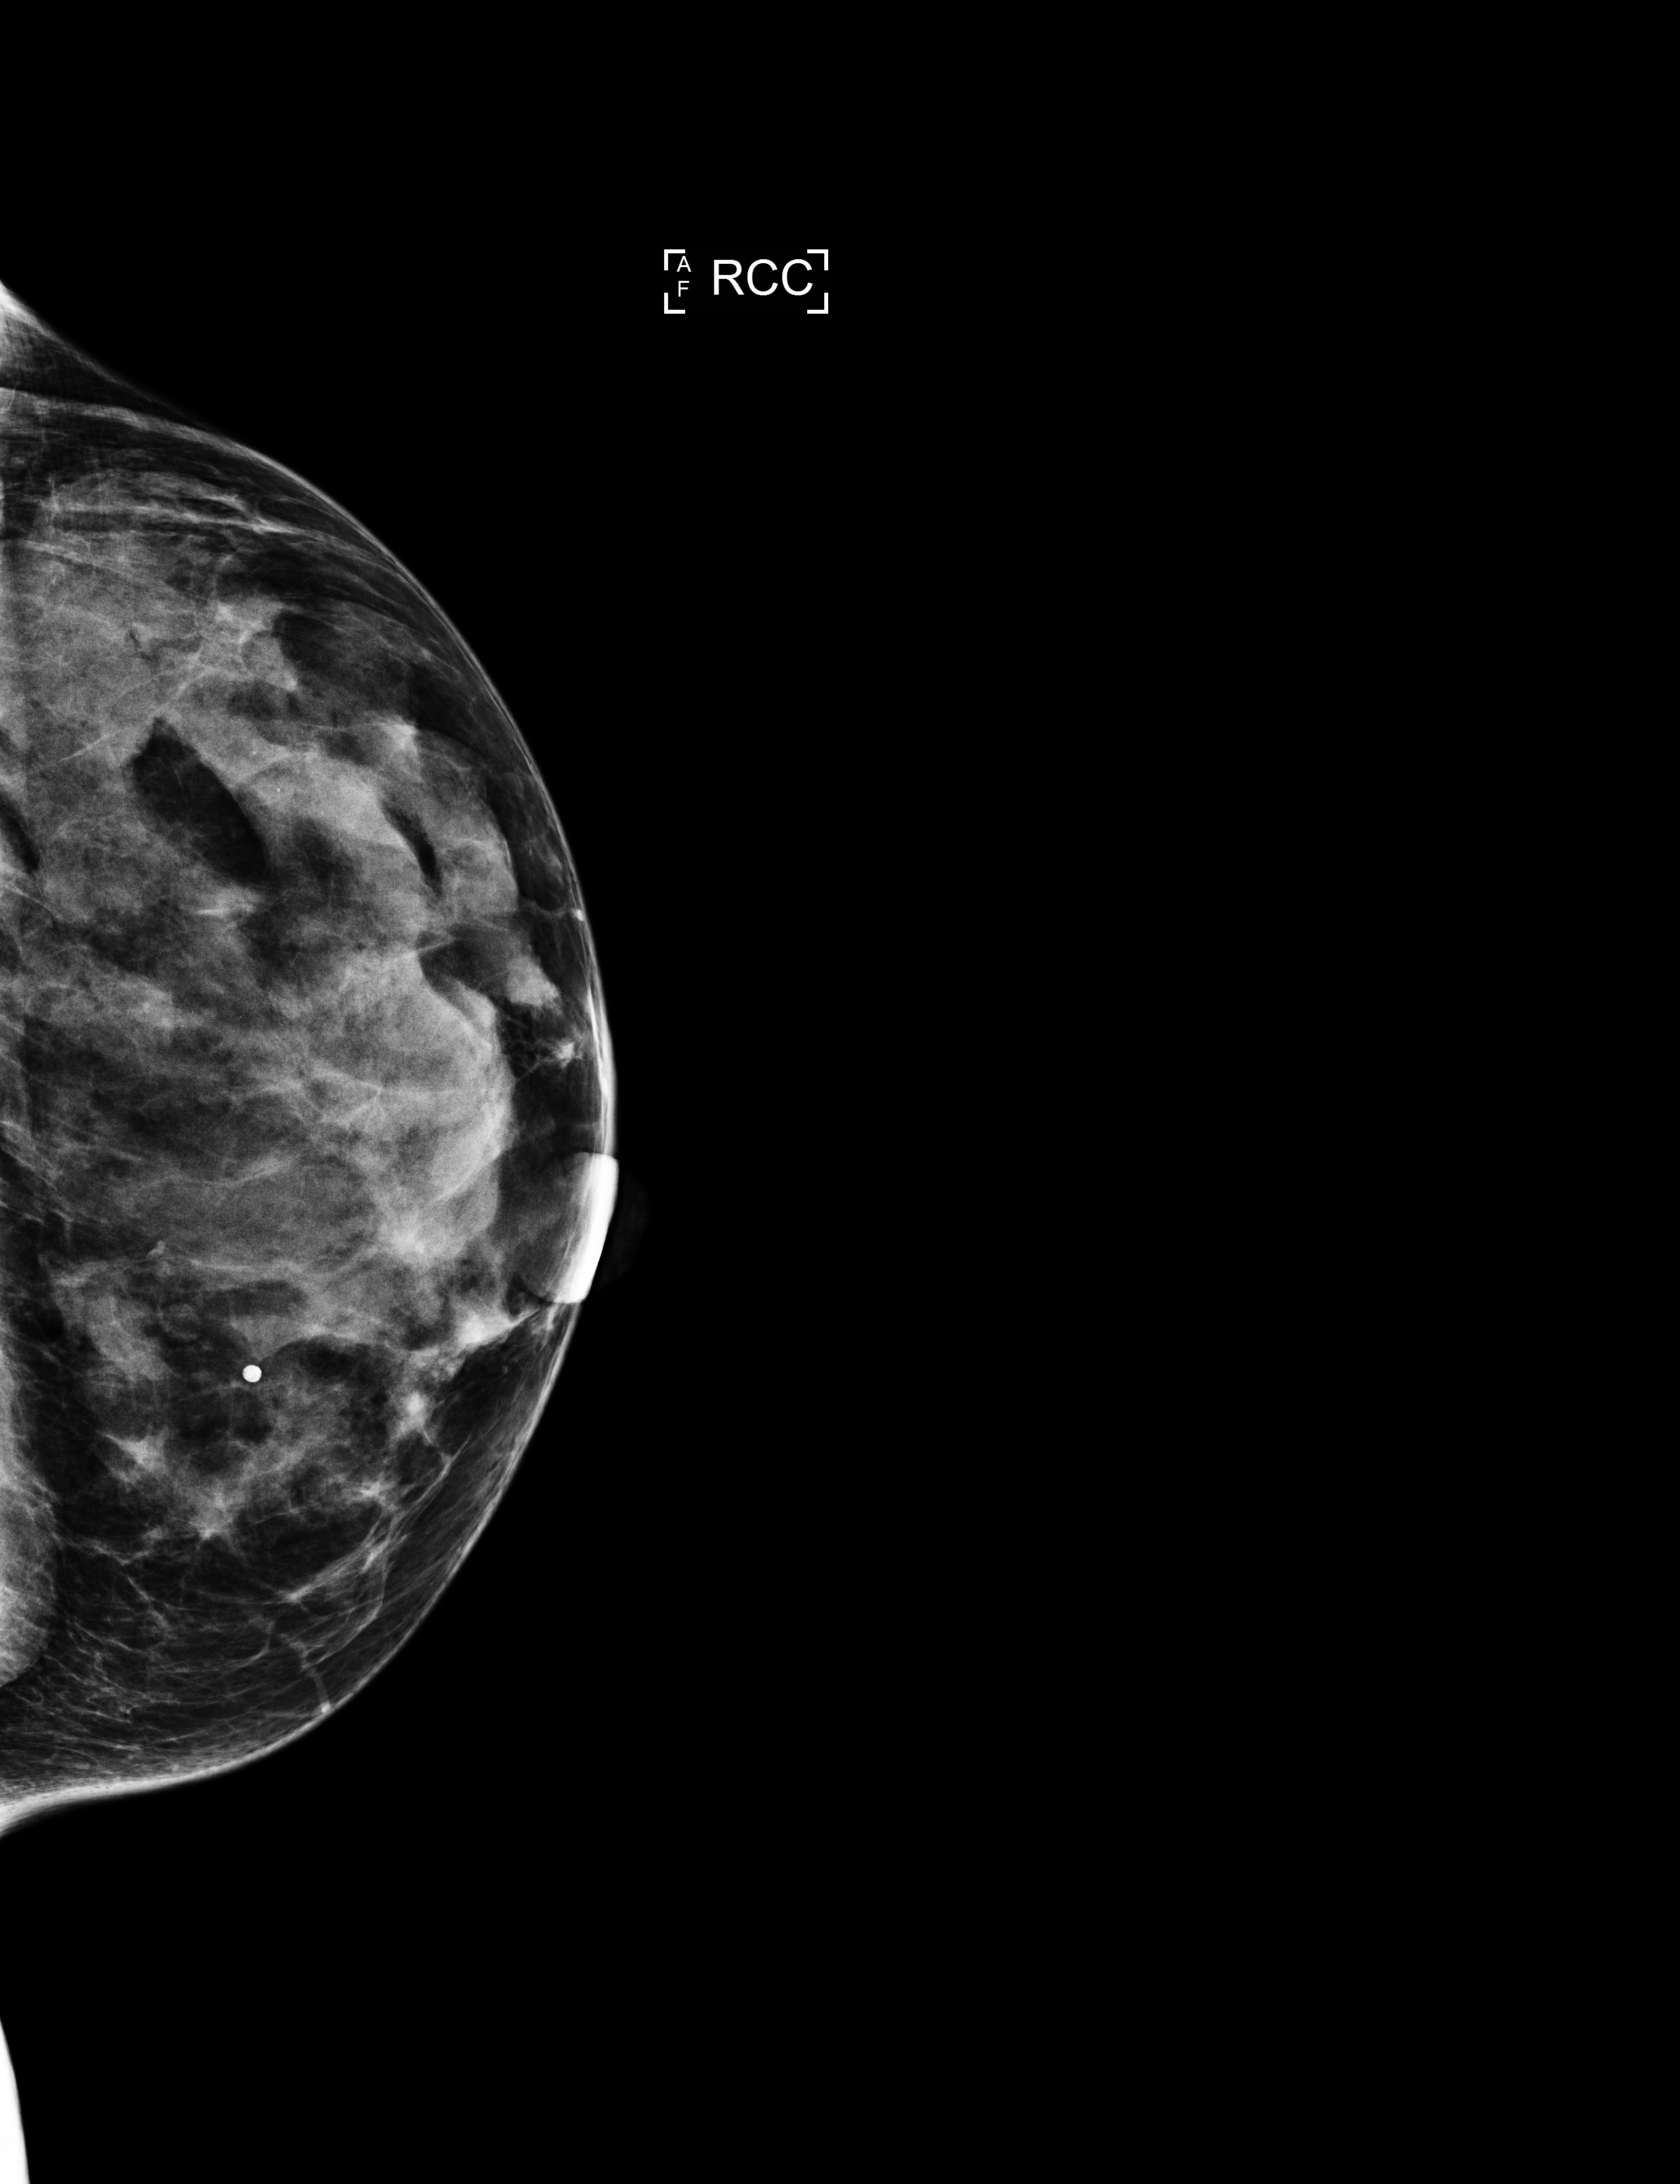
Full-field digital mammogram (FFDM), right breast, craniocaudal (CC) view, annual screening mammography examination. Patient: female, 53 years.
Breast density at the screening exam (both breasts): heterogeneously dense (BI-RADS density category c). Final BI-RADS assessment for this screening round (tomosynthesis exam, both breasts): category 1. Recall: no recall after this screen.